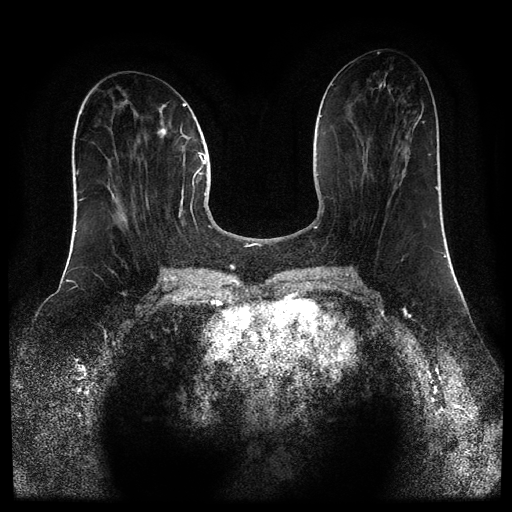
Breast MRI (dynamic contrast-enhanced, multi-phase), one axial slice; slice 37 of 110 in the series (ordered by position); dynamic contrast-enhanced series, time point 2 of 5 at this slice position (early post-contrast); 1.5 T; TE 2.6 ms, TR 5.4 ms; 2 mm slice thickness; 512 × 512 image matrix. Patient: female, 43 years.
Annotated regions visible in this slice (semi-automatically segmented with operator editing):
- breast lesion (labelled 'tumour' in the annotation; benign lesions carry a separate 'benign' label): bounding box [x1, y1, x2, y2] px = [157, 125, 167, 138]